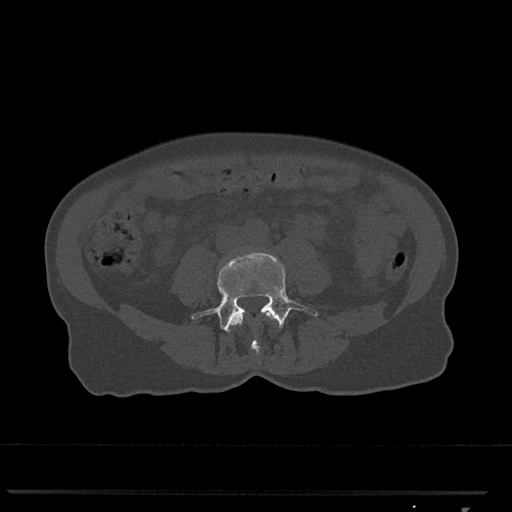
CT including the spine, one axial slice. Position 226 of 793 along the scan axis. Bone window (W 1800 / L 400 HU). 512 × 512 image matrix, field of view 380 × 380 mm. Female patient, age 62 years. From the clinical record (not read from this slice): primary cancer: renal.
Outlined on this slice (semi-automatically segmented with operator editing):
- L3 vertebra: bounding box <230,313,274,354> (left, top, right, bottom; pixels)
- L4 vertebra: <191,253,318,333>